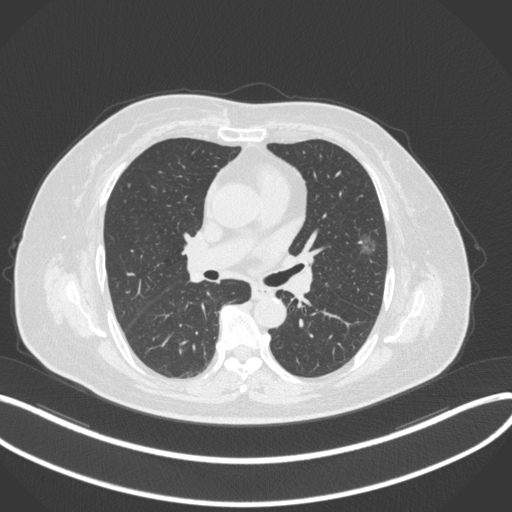
Chest CT, one axial slice. Slice 174 of 286 in the series (ordered by position). Reconstruction kernel B31f. Lung window (W 1500 / L -600 HU). 1 mm slice thickness. 512 × 512 image matrix, field of view 400 × 400 mm. Female patient, age 76 years. From the clinical record (not read from this slice): clinical TNM (as recorded): T1b N0 M0.
Outlined on this slice (bounding box drawn by a radiologist):
- lung tumour (recorded histology: adenocarcinoma): box from (x=354, y=226) to (x=380, y=257) px